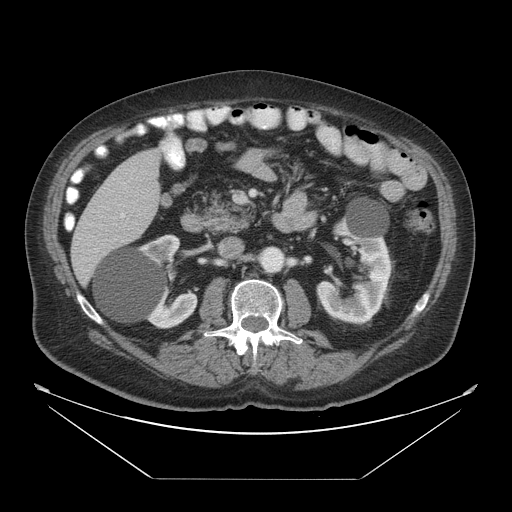
Contrast-enhanced abdominal CT, one axial slice. Position 18 of 45 along the scan axis. Reconstruction kernel STANDARD. 120 kVp. Intravenous contrast given. Soft-tissue window (W 400 / L 40 HU). 512 × 512 image matrix, field of view 463 × 463 mm. Male patient, age 87 years. From the clinical record (not read from this slice): diagnosis: colorectal cancer liver metastases, imaged before liver resection; multiple liver metastases: no; largest metastasis: 4.5 cm.
Structures marked on this image (outlined manually by an expert reader):
- liver: bounding box (x1, y1, x2, y2) in pixels: (70, 150, 162, 287)
- portal vein (with intrahepatic branches): (120, 213, 125, 218)